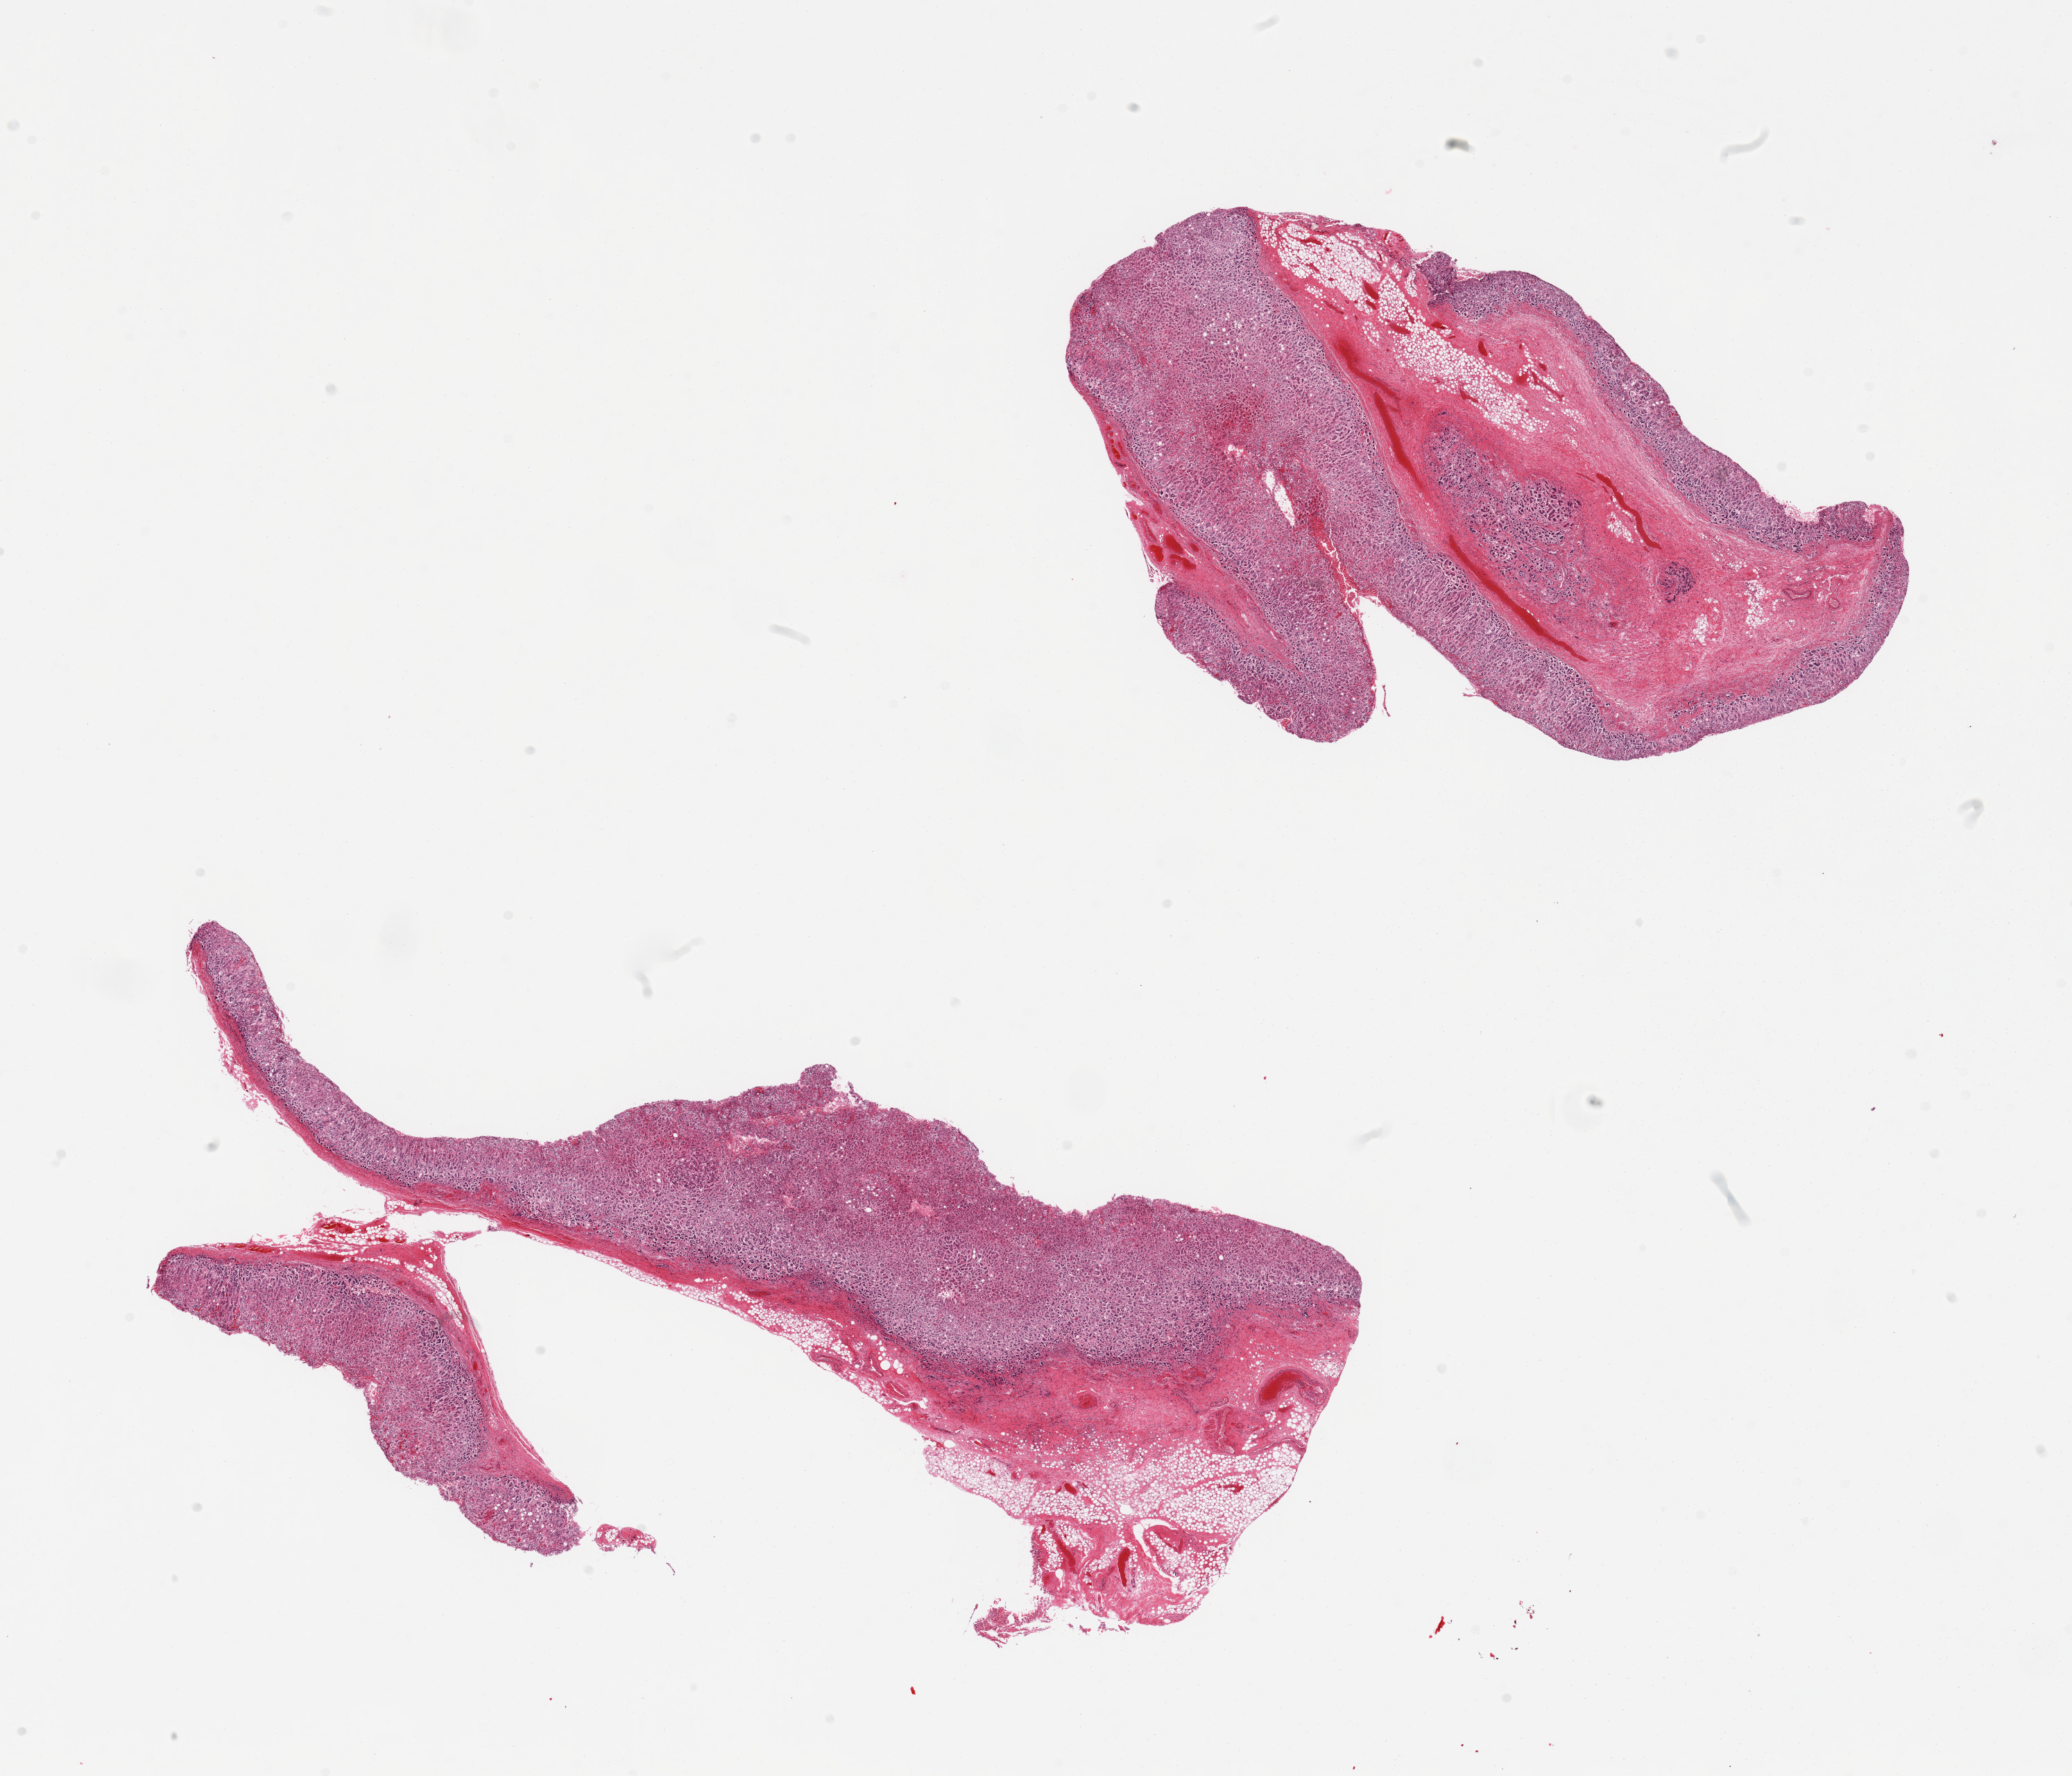
Whole-slide image, H&E stain — whole scanned area (about 23.6 x 20.2 mm, slide scanned at 20x) shown as a low-resolution overview; PAXgene-fixed paraffin-embedded (PFPE) section; sampled site (target tissue): adrenal gland; donor tissue sample. Donor: male.
Reviewer comment on this tissue sample: 2 pieces, both with ~30% fat and fibrous tissue.